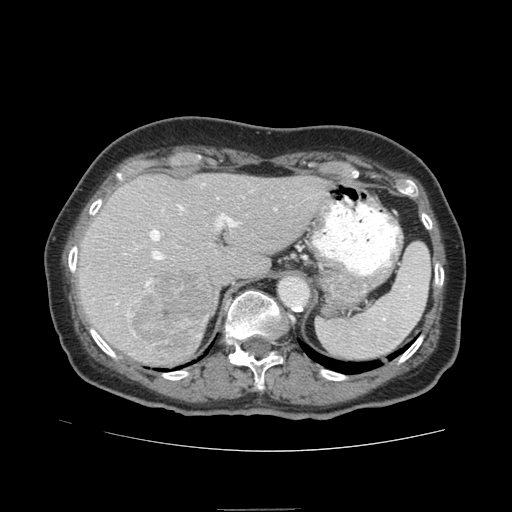
Contrast-enhanced abdominal CT (liver protocol), one axial slice; slice 56 of 95 in the series (ordered by position); reconstruction kernel STANDARD; soft-tissue window (W 400 / L 40 HU); 2.5 mm slice thickness; 512 × 512 image matrix, field of view 360 × 360 mm. From the clinical record (not read from this slice): diagnosis: hepatocellular carcinoma (patient treated with transarterial chemoembolisation; whether this scan precedes or follows treatment is not stated here); TNM stage (as recorded): Stage-IVA; Child-Pugh class: B; tumour differentiation: moderately differentiated.
Structures marked on this image (semi-automatic segmentation, software-assisted and operator-edited):
- liver parenchyma outside the tumour (the mass and vessels are separate outlines, so this box may not span the whole liver): box from (x=76, y=174) to (x=330, y=366) px
- mass: (x=125, y=270)–(x=218, y=359)
- liver vessels: (x=117, y=184)–(x=276, y=305)